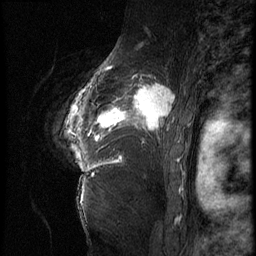
Breast MRI (dynamic contrast-enhanced), one sagittal slice. Slice 51 of 62 in the series (ordered by position). 3 images stored at this slice position (order not interpretable as contrast timing). 1.5 T. TE 4.2 ms, TR 9 ms. 256 × 256 image matrix, field of view 180 × 180 mm. Patient: female, 56 years. Case-level facts recorded for this patient, not image findings: setting: breast cancer imaged before/during neoadjuvant chemotherapy; receptor status: HER2-positive.
Annotated regions visible in this slice (semi-automatically segmented with operator editing):
- analysis volume of interest (the breast-tissue region the enhancement analysis was run in; not a lesion): box from (x=84, y=75) to (x=181, y=153) px
- tumour enhancement mask (voxels above the 140 % enhancement threshold inside the analysis volume of interest): (x=90, y=83)–(x=175, y=141)